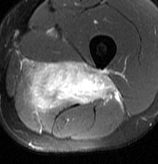
MRI of an extremity soft-tissue mass, one axial slice; slice 42 of 70 in the series (ordered by position); T2-weighted fat-saturated; MR volume resampled by the dataset authors to the PET/CT grid (not the native acquisition matrix); 3.27 mm slice thickness; 158 × 164 image matrix, field of view 154 × 160 mm. Male patient. Case-level facts recorded for this patient, not image findings: histological type: extraskeletal osteosarcoma; grade: high; site of the primary tumour: left adductur.
Outlined on this slice (expert contour drawn on MRI and transferred to this co-registered scan by the dataset authors):
- gross tumour volume (mass): box from (x=22, y=60) to (x=121, y=111) px